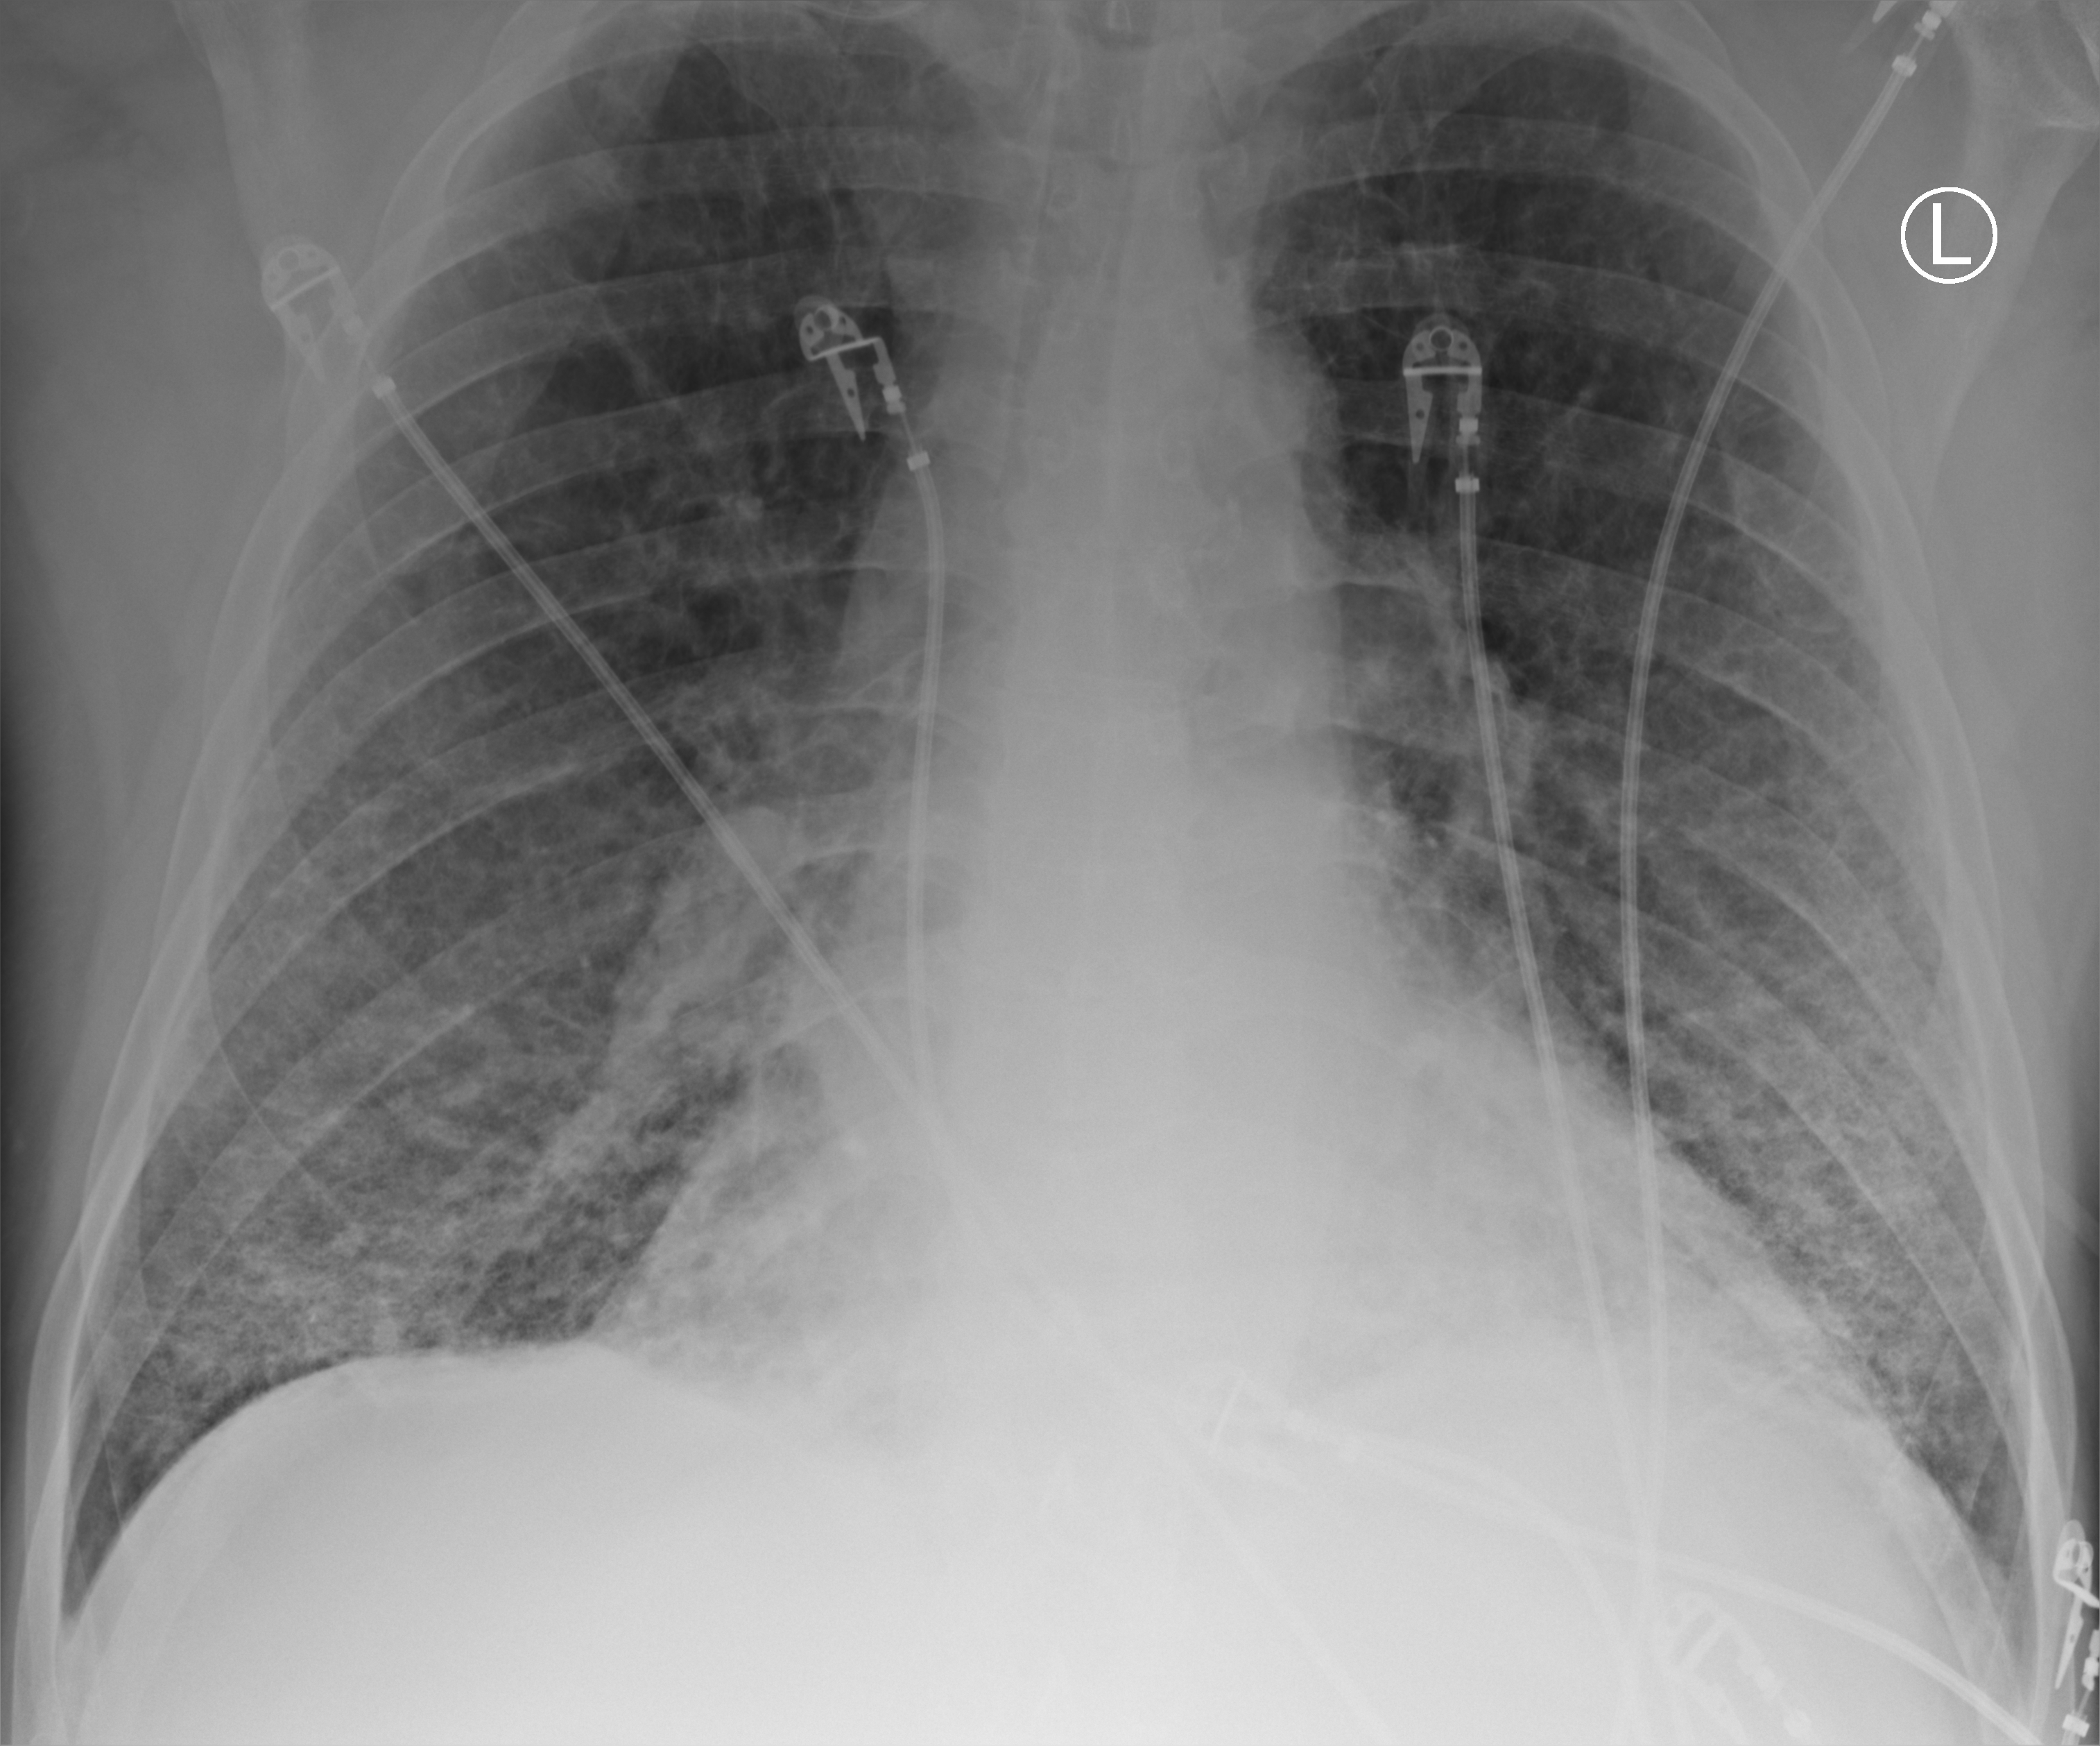
Chest X-ray (portable). Patient hospitalised with COVID-19, aged 18–59 years.
Admission-level facts for this patient (not findings on this image; timing relative to this image not recorded): mechanically ventilated during this hospital stay: no; length of hospital stay: 3 days; COPD (admission record): yes.